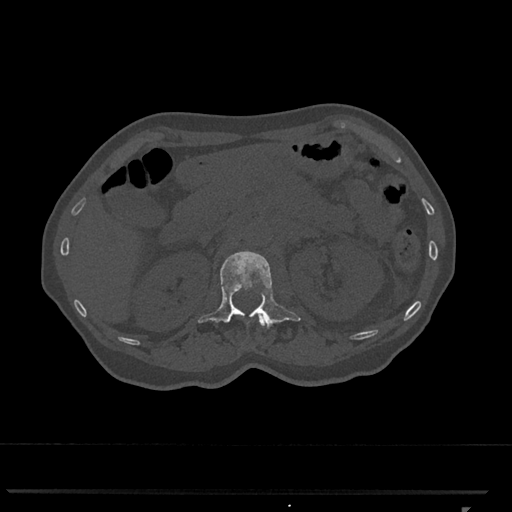
CT including the spine, one axial slice; position 410 of 793 along the scan axis; bone window (W 1800 / L 400 HU); 0.5 mm slice thickness; 512 × 512 image matrix, field of view 380 × 380 mm. Patient: female, 62 years. Case-level facts recorded for this patient, not image findings: primary cancer: renal.
Outlined on this slice (semi-automatically segmented with operator editing):
- L1 vertebra: box from (x=198, y=251) to (x=301, y=328) px
- T12 vertebra: (x=259, y=316)–(x=265, y=326)